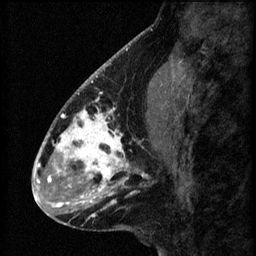
Breast MRI (dynamic contrast-enhanced), one sagittal slice. Position 24 of 60 along the scan axis. 3 images stored at this slice position (order not interpretable as contrast timing). 1.5 T. TE 4.2 ms, TR 8.2 ms. 2.2 mm slice thickness. 256 × 256 image matrix. Patient: female, 41 years.
Outlined on this slice (semi-automatically segmented with operator editing):
- analysis volume of interest (the breast-tissue region the enhancement analysis was run in; not a lesion): bounding box (x1, y1, x2, y2) in pixels: (56, 104, 157, 207)
- tumour enhancement mask (voxels above the 70 % enhancement threshold inside the analysis volume of interest): (56, 108, 148, 207)